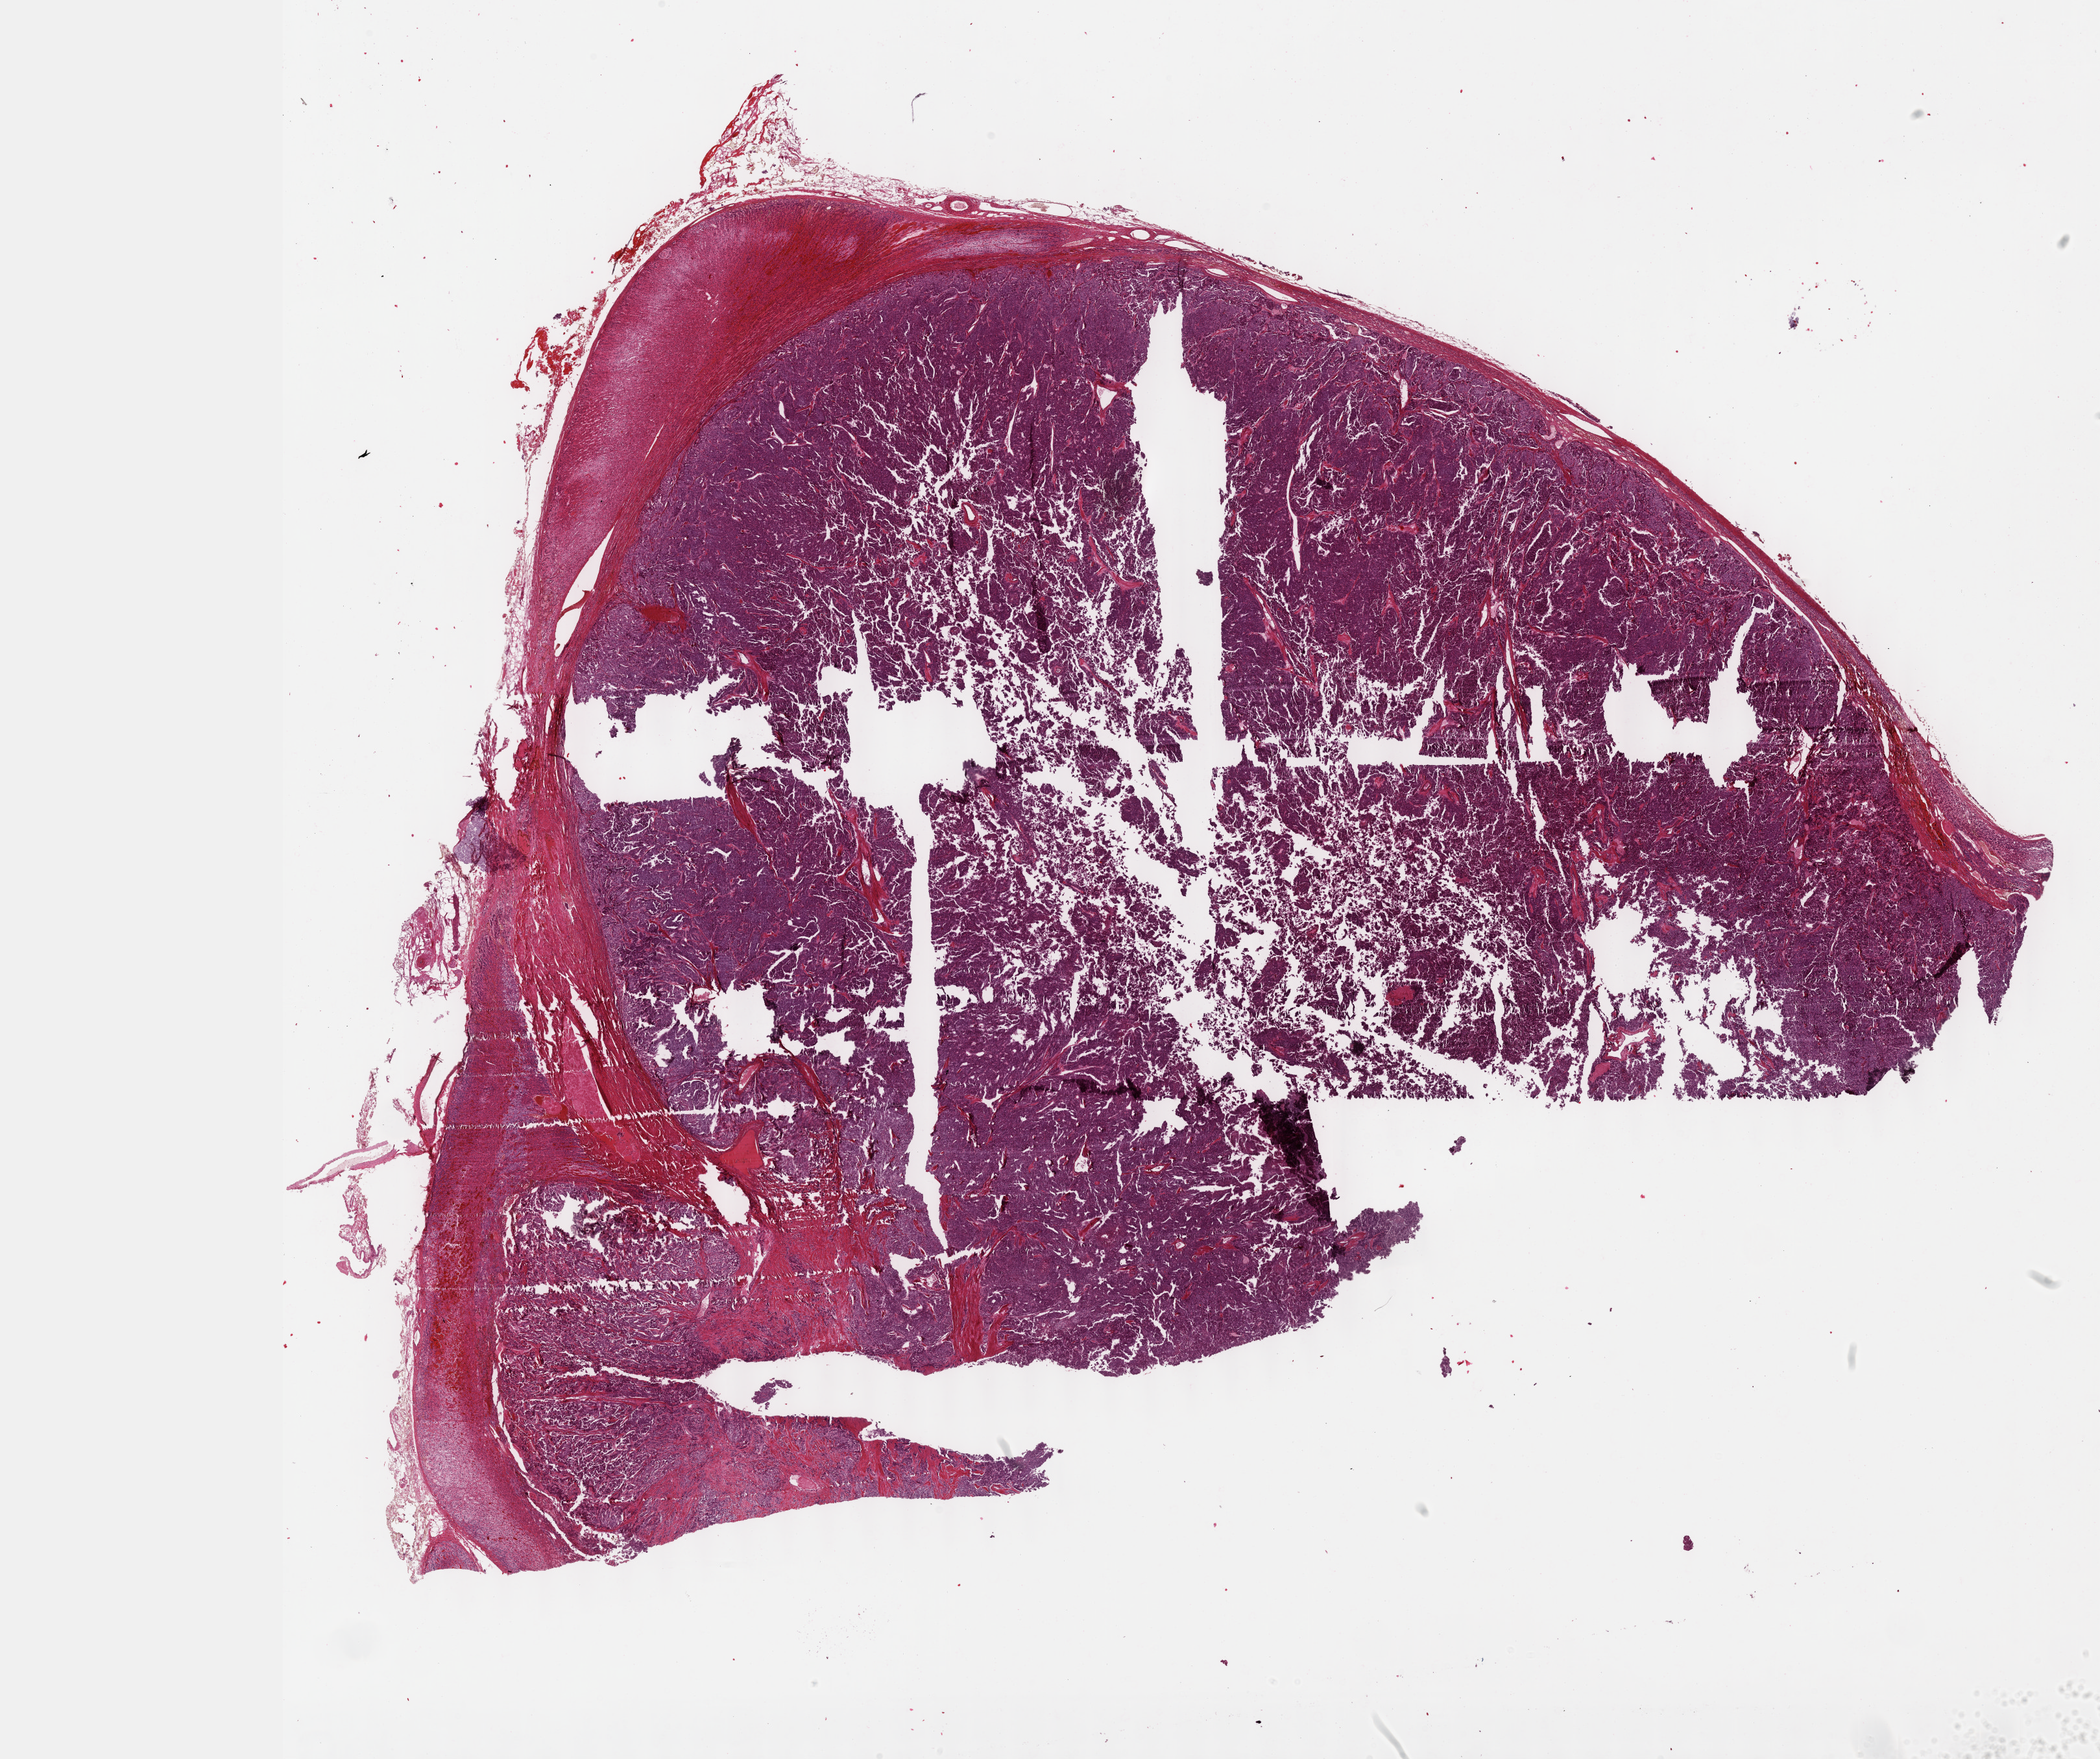
Digitized H&E tissue section (whole slide) — shown as a low-resolution overview of the whole scanned area (about 26.2 x 21.9 mm, from a 40x scan). FFPE section. Sample: primary tumour, adrenal gland. Patient: male, age at initial diagnosis 27 years.
• pathologic diagnosis: Pheochromocytoma, NOS
• laterality: right